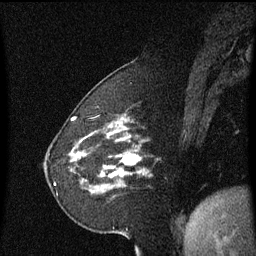
Breast MRI (dynamic contrast-enhanced), one sagittal slice; position 16 of 60 along the scan axis; dynamic contrast-enhanced series, image 2 of 3 at this slice position (ordered by acquisition); 1.5 T; TE 4.2 ms, TR 8.4 ms; 2.2 mm slice thickness; 256 × 256 image matrix, field of view 200 × 200 mm. Female patient, age 60 years. Case-level facts recorded for this patient, not image findings: setting: breast cancer imaged before/during neoadjuvant chemotherapy; receptor status: triple-negative.
Annotated regions visible in this slice (semi-automatic segmentation, software-assisted and operator-edited):
- analysis volume of interest (the breast-tissue region the enhancement analysis was run in; not a lesion): bounding box <70,142,139,193> (left, top, right, bottom; pixels)
- tumour enhancement mask (voxels above the 70 % enhancement threshold inside the analysis volume of interest): <103,154,139,179>